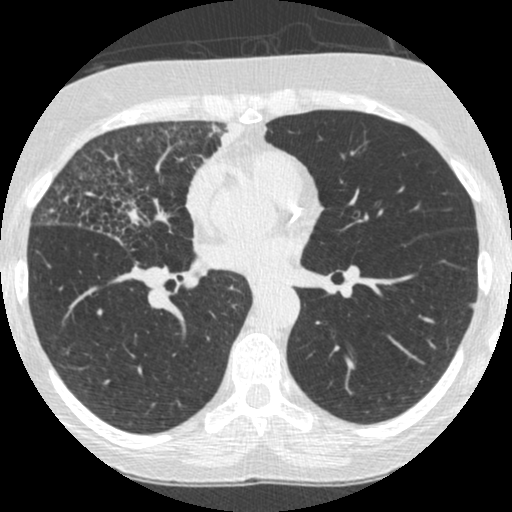
Low-dose screening chest CT, one axial slice. Position 129 of 253 along the scan axis. 120 kVp. Lung window (W 1500 / L -600 HU). 1.25 mm slice thickness. 512 × 512 image matrix, field of view 294 × 294 mm.
Structures marked on this image (expert manual segmentation):
- lesion 4 (tumor, upper lobe of right lung): bounding box (x1, y1, x2, y2) in pixels: (206, 120, 242, 158)